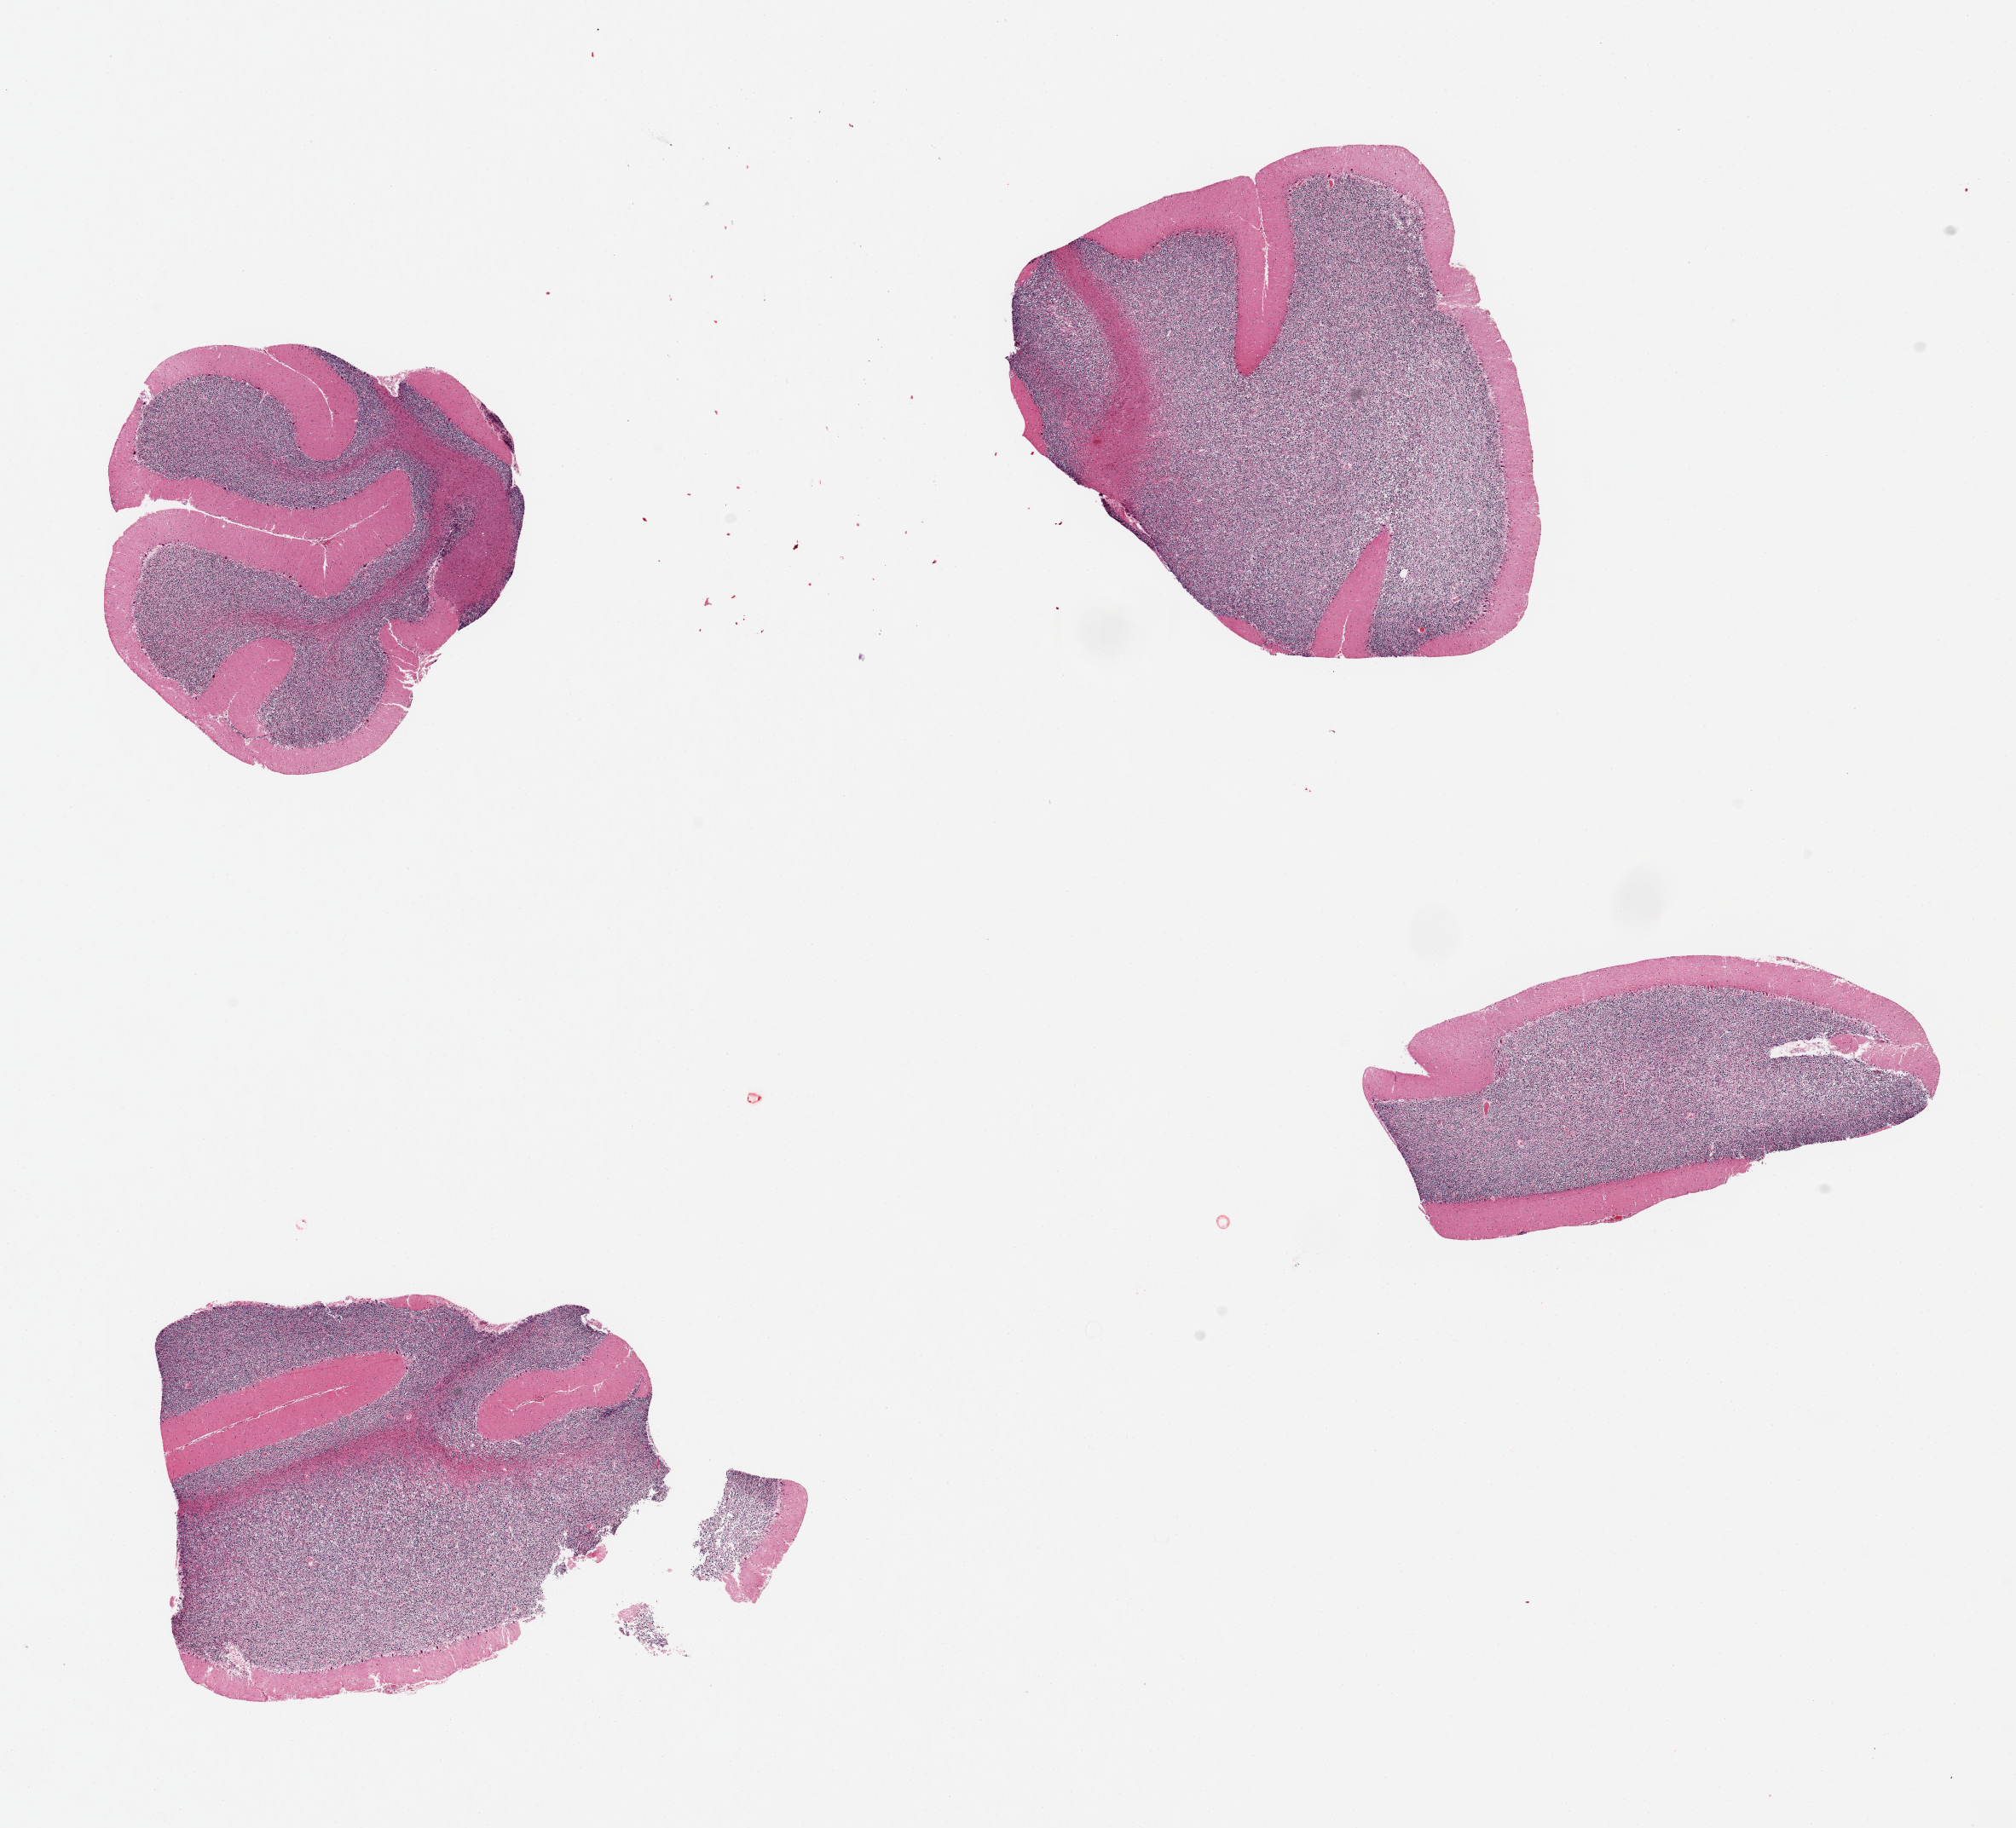
H&E whole-slide image — low-resolution overview of the scanned area, about 18.7 x 17.0 mm. PAXgene-fixed, paraffin-embedded tissue. Section of cerebellum (target tissue). Donor tissue sample. Donor sex: male.
- pathologist's review note for this sample: 4 pieces, ~5x4mm. Granular layer poorly preserved